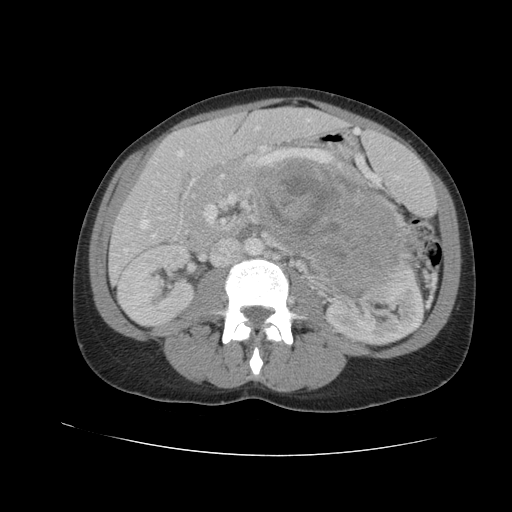
Contrast-enhanced abdominal CT, one axial slice. Slice 53 of 90 in the series (ordered by position). Reconstruction kernel STANDARD. Intravenous contrast given. Soft-tissue window (W 400 / L 40 HU). 512 × 512 image matrix, field of view 360 × 360 mm. Female patient. Case-level facts recorded for this patient, not image findings: diagnosis: adrenocortical carcinoma; tumour side: left adrenal; tumour size at pathology: 18 cm; Ki-67 index: 11 %.
Outlined on this slice (semi-automatically segmented with operator editing):
- mass: bounding box [x1, y1, x2, y2] px = [258, 160, 406, 290]